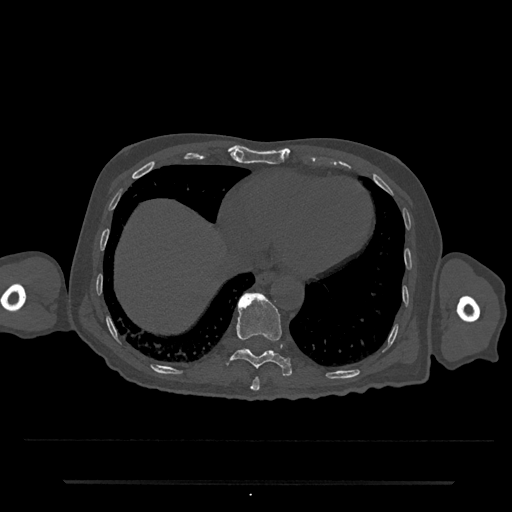
CT including the spine, one axial slice. Position 311 of 797 along the scan axis. Reconstruction kernel Br40s/3. Bone window (W 1800 / L 400 HU). 512 × 512 image matrix, field of view 427 × 427 mm. Patient: male, 74 years. Case-level facts recorded for this patient, not image findings: primary cancer: prostate.
Annotated regions visible in this slice (semi-automatically segmented with operator editing):
- T10 vertebra: box from (x=225, y=293) to (x=292, y=377) px
- T9 vertebra: (x=250, y=377)–(x=260, y=391)